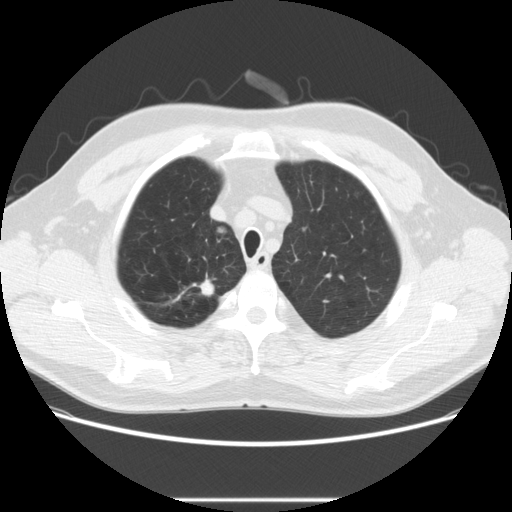
Axial slice from a low-dose chest CT screening exam, baseline screening round, lung window (W 1500 / L -600 HU), 2.5 mm slice thickness, standard (soft-tissue) reconstruction kernel (STANDARD), 120 kVp, slice 41 of 270 in the series, 512 × 512 image matrix. Male, age 64 years at enrolment. Former smoker at enrolment.
2 lesions marked by an expert reader on this slice (largest first), bounding box [x1, y1, x2, y2] px = [172, 277, 222, 307]; [212, 220, 236, 245]. The screening reader recorded 2 non-calcified nodules or masses ≥4 mm on this exam (right upper lobe, right upper lobe); which of them these boxes mark is not recorded. Official screen result: positive, change unspecified: nodule(s) >= 4 mm or enlarging nodule(s), mass(es), or other non-specific abnormalities suspicious for lung cancer. Participant outcome: lung cancer diagnosed 753 days after this screen — adenocarcinoma, NOS, right upper lobe, moderately differentiated (G2), stage IA (AJCC 6th edition), 14 mm at pathology.